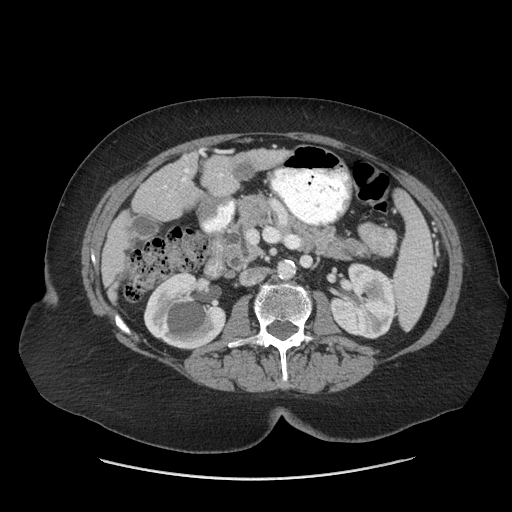
Contrast-enhanced abdominal CT (liver protocol), one axial slice. Slice 20 of 69 in the series (ordered by position). Reconstruction kernel STANDARD. Soft-tissue window (W 400 / L 40 HU). 2.5 mm slice thickness. 512 × 512 image matrix, field of view 420 × 420 mm. Case-level facts recorded for this patient, not image findings: diagnosis: hepatocellular carcinoma (patient treated with transarterial chemoembolisation; whether this scan precedes or follows treatment is not stated here); TNM stage (as recorded): Stage-IIIB; Child-Pugh class: A; tumour differentiation: moderately differentiated; tumour nodularity: multinodular.
Annotated regions visible in this slice (semi-automatically segmented with operator editing):
- liver parenchyma outside the tumour (the mass and vessels are separate outlines, so this box may not span the whole liver): bounding box [x1, y1, x2, y2] px = [102, 148, 288, 300]
- liver vessels: [184, 151, 230, 176]